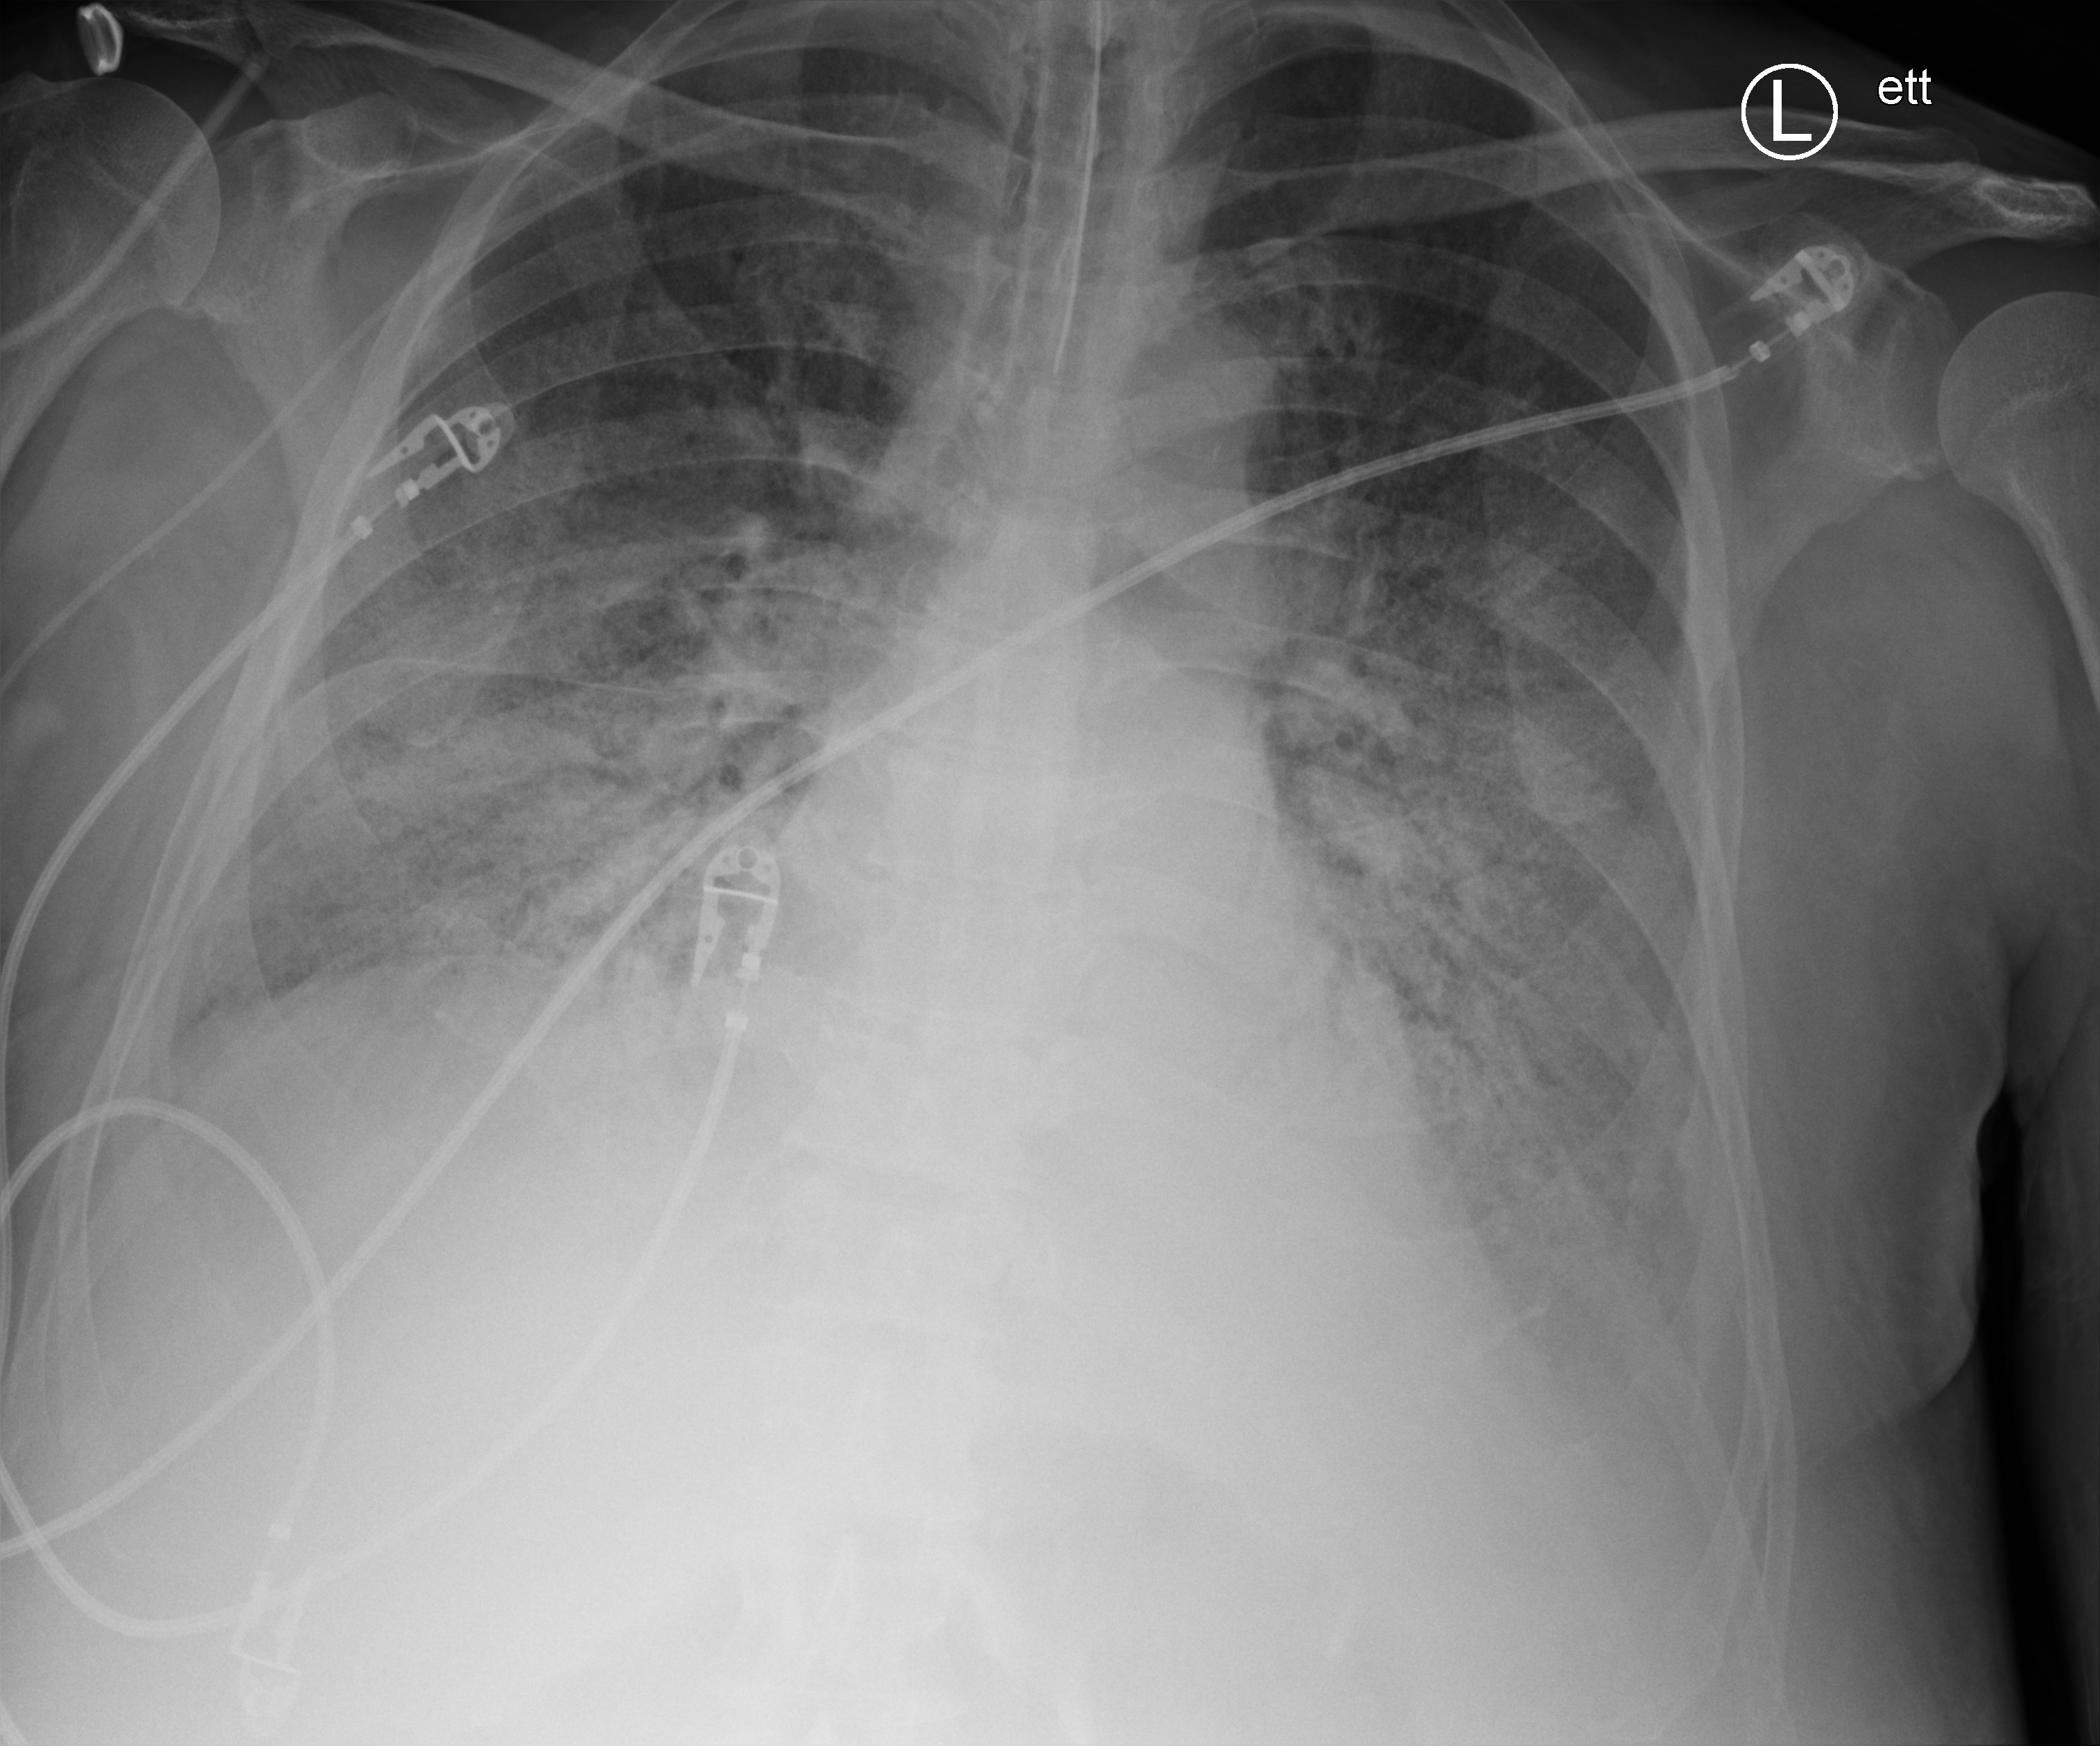
Bedside chest radiograph (computed radiography), anteroposterior (AP) projection. Male patient hospitalised with COVID-19, age 60–74 years.
Admission-level facts for this patient (not findings on this image; timing relative to this image not recorded):
- COPD (admission record): no